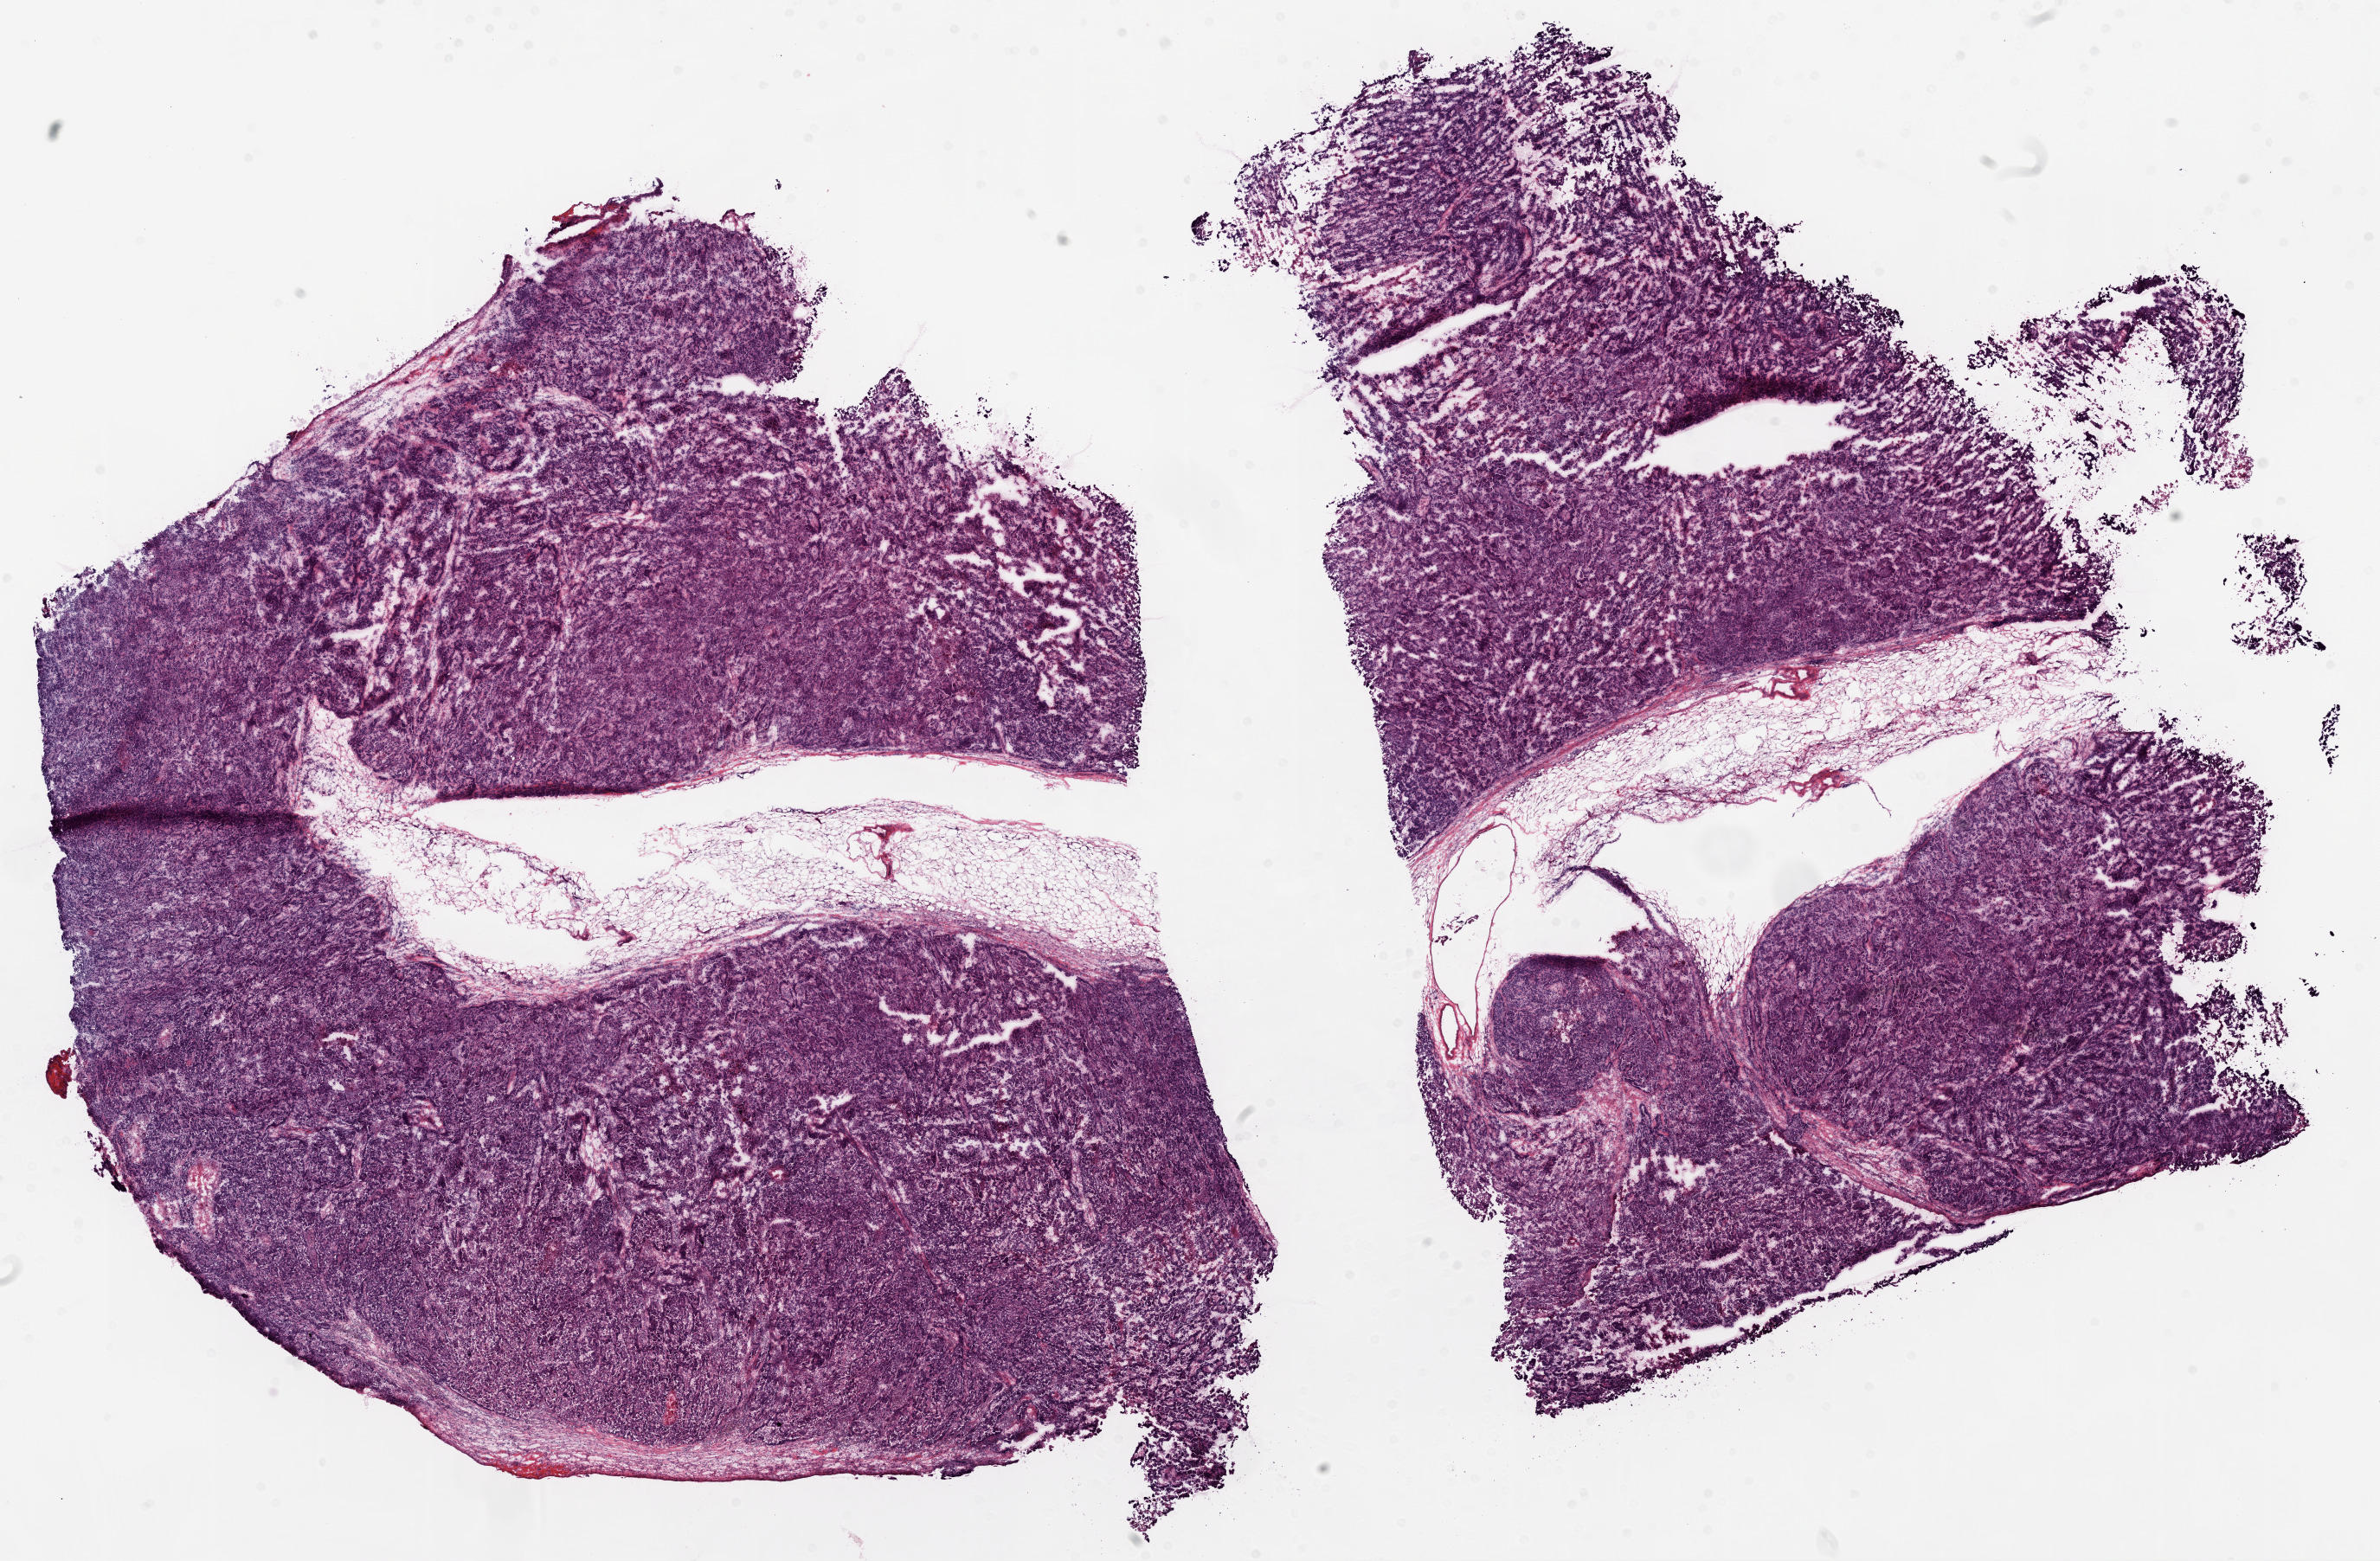
H&E-stained whole-slide image — a low-resolution overview of the entire scanned area, about 22.1 x 14.5 mm (slide scanned at 20x), frozen section from the top of the tissue portion, ovary, primary tumour sample. Patient: female, age at initial diagnosis 65 years. Histologic grade: G3 (poorly differentiated). Pathologist review of this section (percent, as recorded): tumour cells 94%, tumour nuclei 99%, normal cells 0%, stromal cells 1%, necrosis 5%.
Histologic diagnosis: Serous cystadenocarcinoma, NOS. Laterality: bilateral. FIGO stage: IIIC.